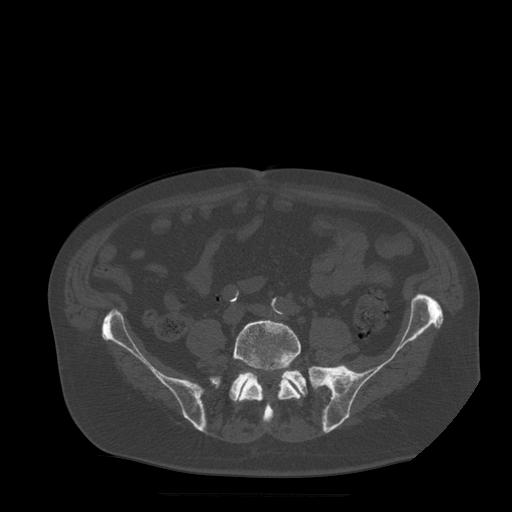
CT including the spine, one axial slice. Bone window (W 1800 / L 400 HU). 1.25 mm slice thickness. 512 × 512 image matrix, field of view 420 × 420 mm. Patient age 72 years. From the clinical record (not read from this slice): primary cancer: prostate.
Annotated regions visible in this slice (semi-automatically segmented with operator editing):
- L5 vertebra: box from (x=233, y=320) to (x=302, y=424) px